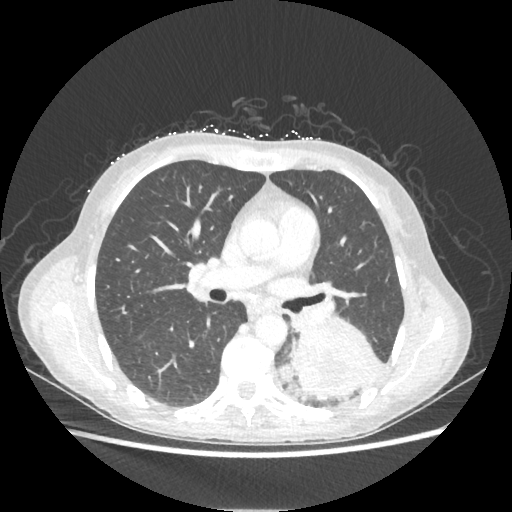
Chest CT, one axial slice; slice 124 of 221 in the series (ordered by position); lung window (W 1500 / L -600 HU); 1.25 mm slice thickness; 512 × 512 image matrix, field of view 360 × 360 mm. Patient: female, 53 years. From the clinical record (not read from this slice): clinical TNM (as recorded): T3 N0 M0.
Annotated regions visible in this slice (rectangle marked by the reading radiologist):
- lung tumour (recorded histology: adenocarcinoma): box from (x=290, y=321) to (x=379, y=398) px